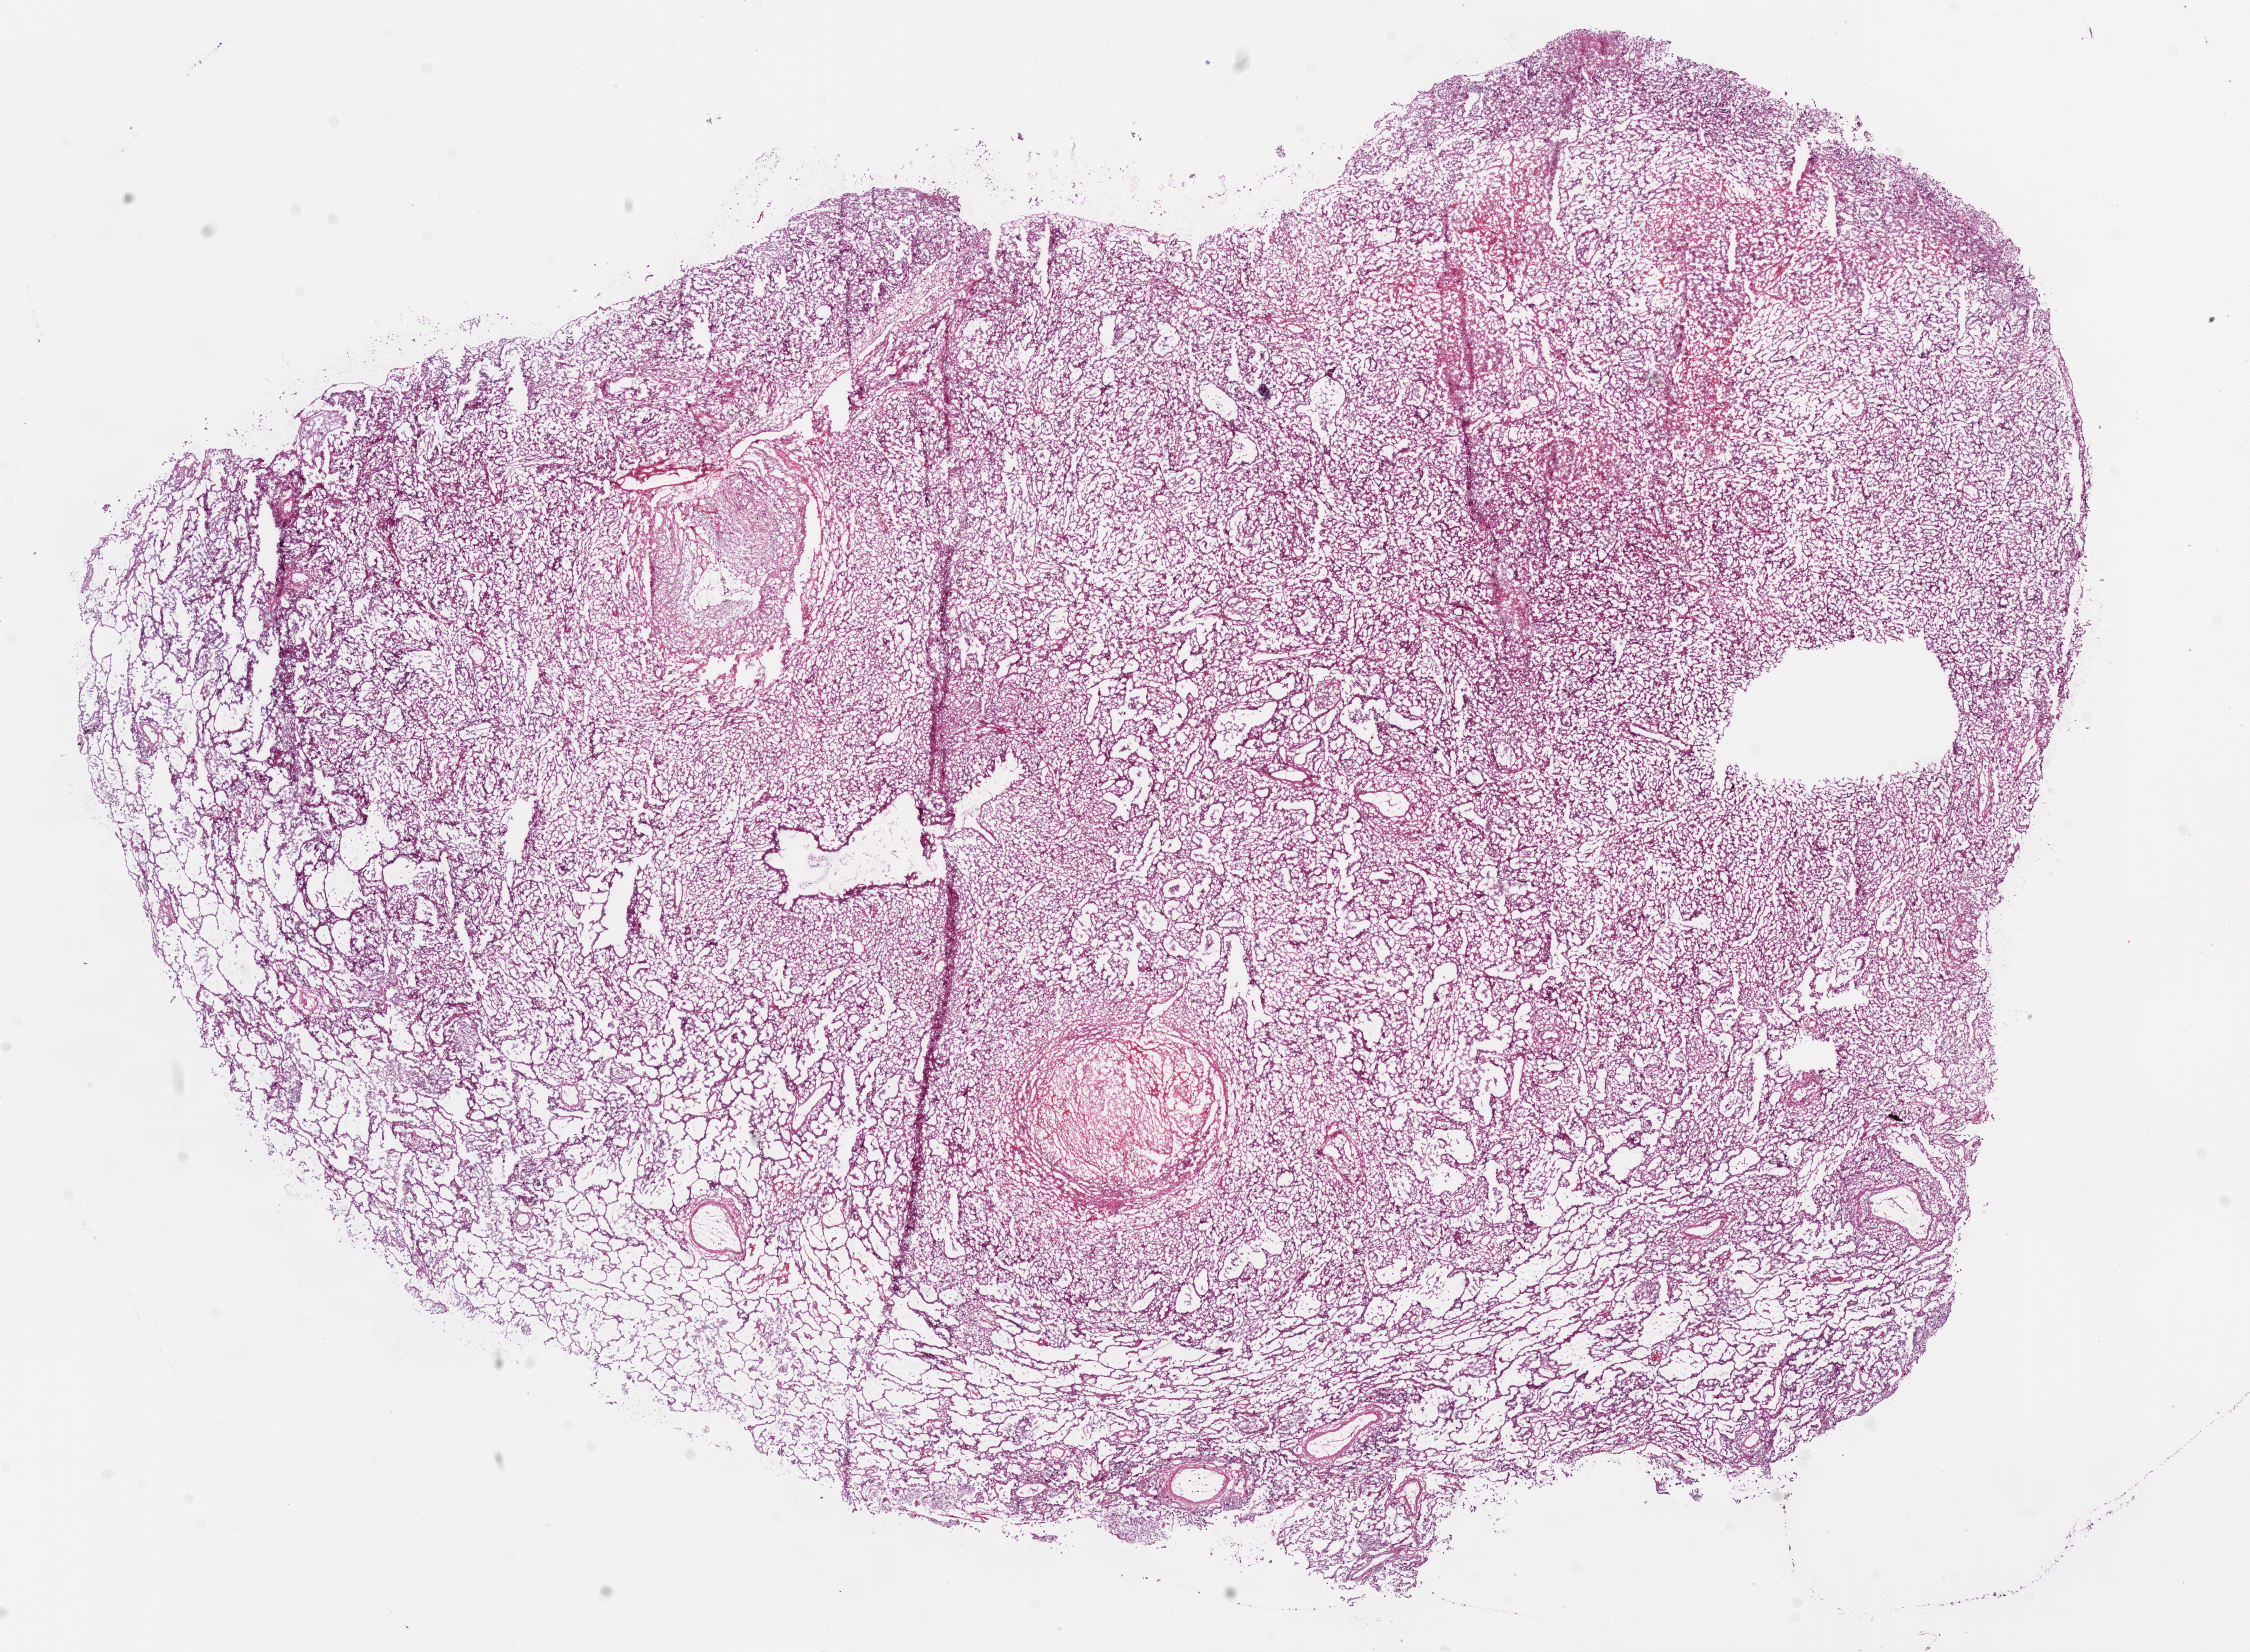
H&E-stained whole-slide image, shown as a low-resolution overview of the whole scanned area (about 18.1 x 13.3 mm, slide scanned at 20x). Frozen section. Sample: primary tumour, lung. Female, age 72 years at initial diagnosis. Composition of this section per pathologist review: tumour cells 80%, tumour nuclei 80%, normal cells 15%, stromal cells 5%, necrosis 0%.
AJCC pathologic stage: IIIB (5th edition). Laterality: right. Diagnosis: Adenocarcinoma, NOS (lower lobe, lung).